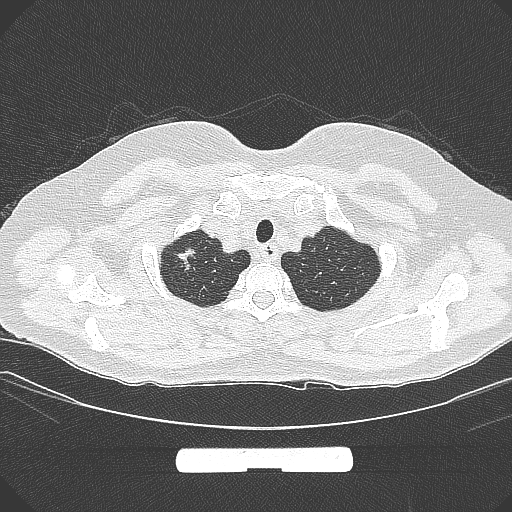
Chest CT, one axial slice. Slice 264 of 295 in the series (ordered by position). Lung window (W 1500 / L -600 HU). 1 mm slice thickness. 512 × 512 image matrix. Patient: female, 58 years. Case-level facts recorded for this patient, not image findings: clinical TNM (as recorded): T1b N0 M0.
Outlined on this slice (bounding box drawn by a radiologist):
- lung tumour (recorded histology: adenocarcinoma): bounding box <169,242,201,277> (left, top, right, bottom; pixels)